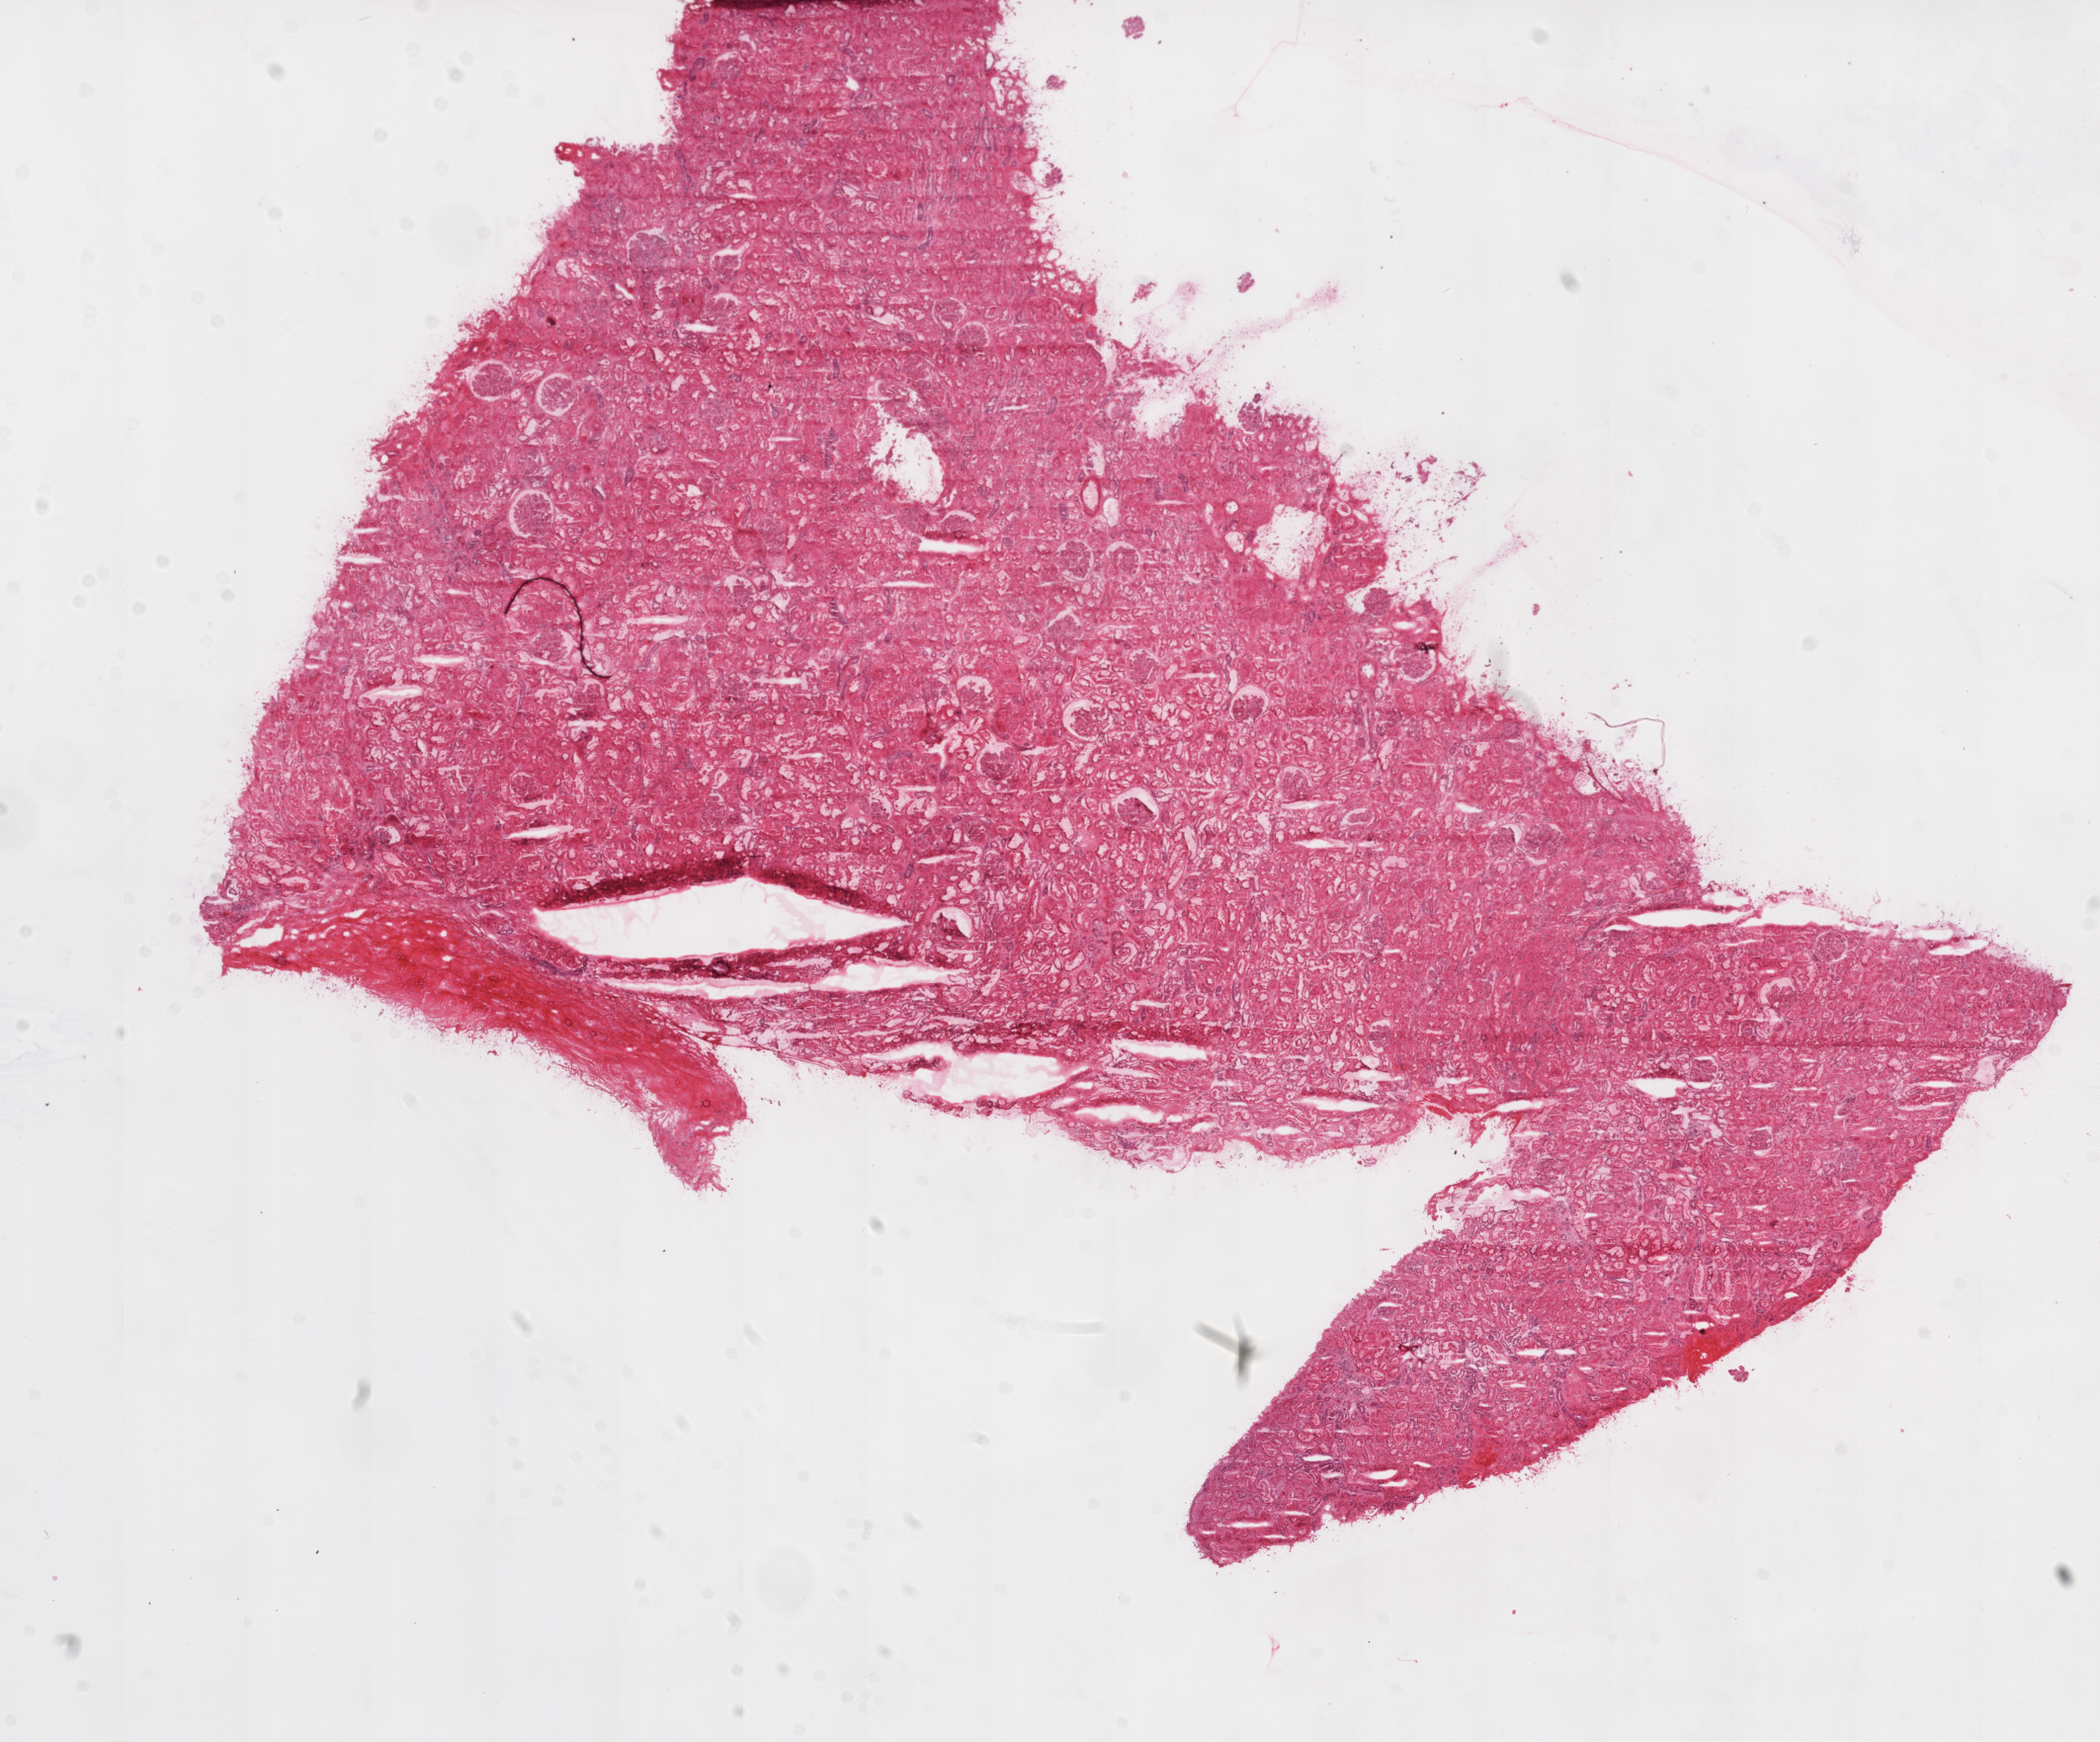
Digitized H&E tissue section (whole slide) — shown as a low-resolution overview of the whole scanned area (about 17.1 x 14.1 mm, from a 20x scan); frozen section from the top of the tissue portion; solid tissue normal (non-tumour tissue) sample from the kidney. Female patient; age at initial diagnosis 47 years.
* this section: solid tissue normal sample (biorepository sample class)
* patient diagnosis: Clear cell adenocarcinoma, NOS